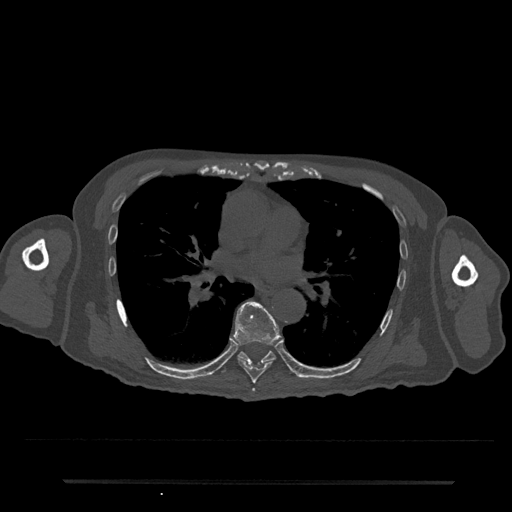
CT including the spine, one axial slice. Position 458 of 797 along the scan axis. Reconstruction kernel Br40s/3. 120 kVp. Bone window (W 1800 / L 400 HU). 0.5 mm slice thickness. 512 × 512 image matrix, field of view 427 × 427 mm. Male patient, age 74 years. Case-level facts recorded for this patient, not image findings: primary cancer: prostate.
Structures marked on this image (semi-automatic segmentation, software-assisted and operator-edited):
- T6 vertebra: bounding box <252,388,255,392> (left, top, right, bottom; pixels)
- T7 vertebra: <233,301,282,384>
- T8 vertebra: <237,351,276,365>